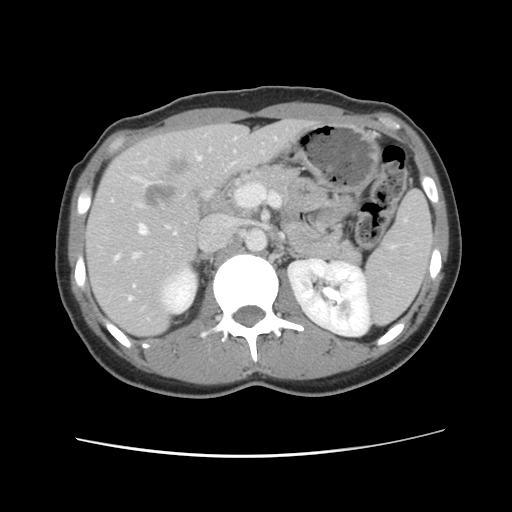
Contrast-enhanced abdominal CT, one axial slice. Slice 57 of 134 in the series (ordered by position). 120 kVp. Intravenous contrast given. Soft-tissue window (W 400 / L 40 HU). 512 × 512 image matrix, field of view 339 × 339 mm. Female patient, age 33 years. From the clinical record (not read from this slice): diagnosis: colorectal cancer liver metastases, imaged before liver resection; multiple liver metastases: yes; largest metastasis: 4.5 cm; disease in both lobes: yes.
Structures marked on this image (expert manual segmentation):
- hepatic veins: bounding box (x1, y1, x2, y2) in pixels: (115, 157, 202, 301)
- liver: (88, 120, 314, 335)
- planned liver remnant (the part of the liver to remain after resection): (88, 120, 313, 336)
- portal vein (with intrahepatic branches): (131, 224, 178, 261)
- liver metastasis: (142, 158, 190, 211)